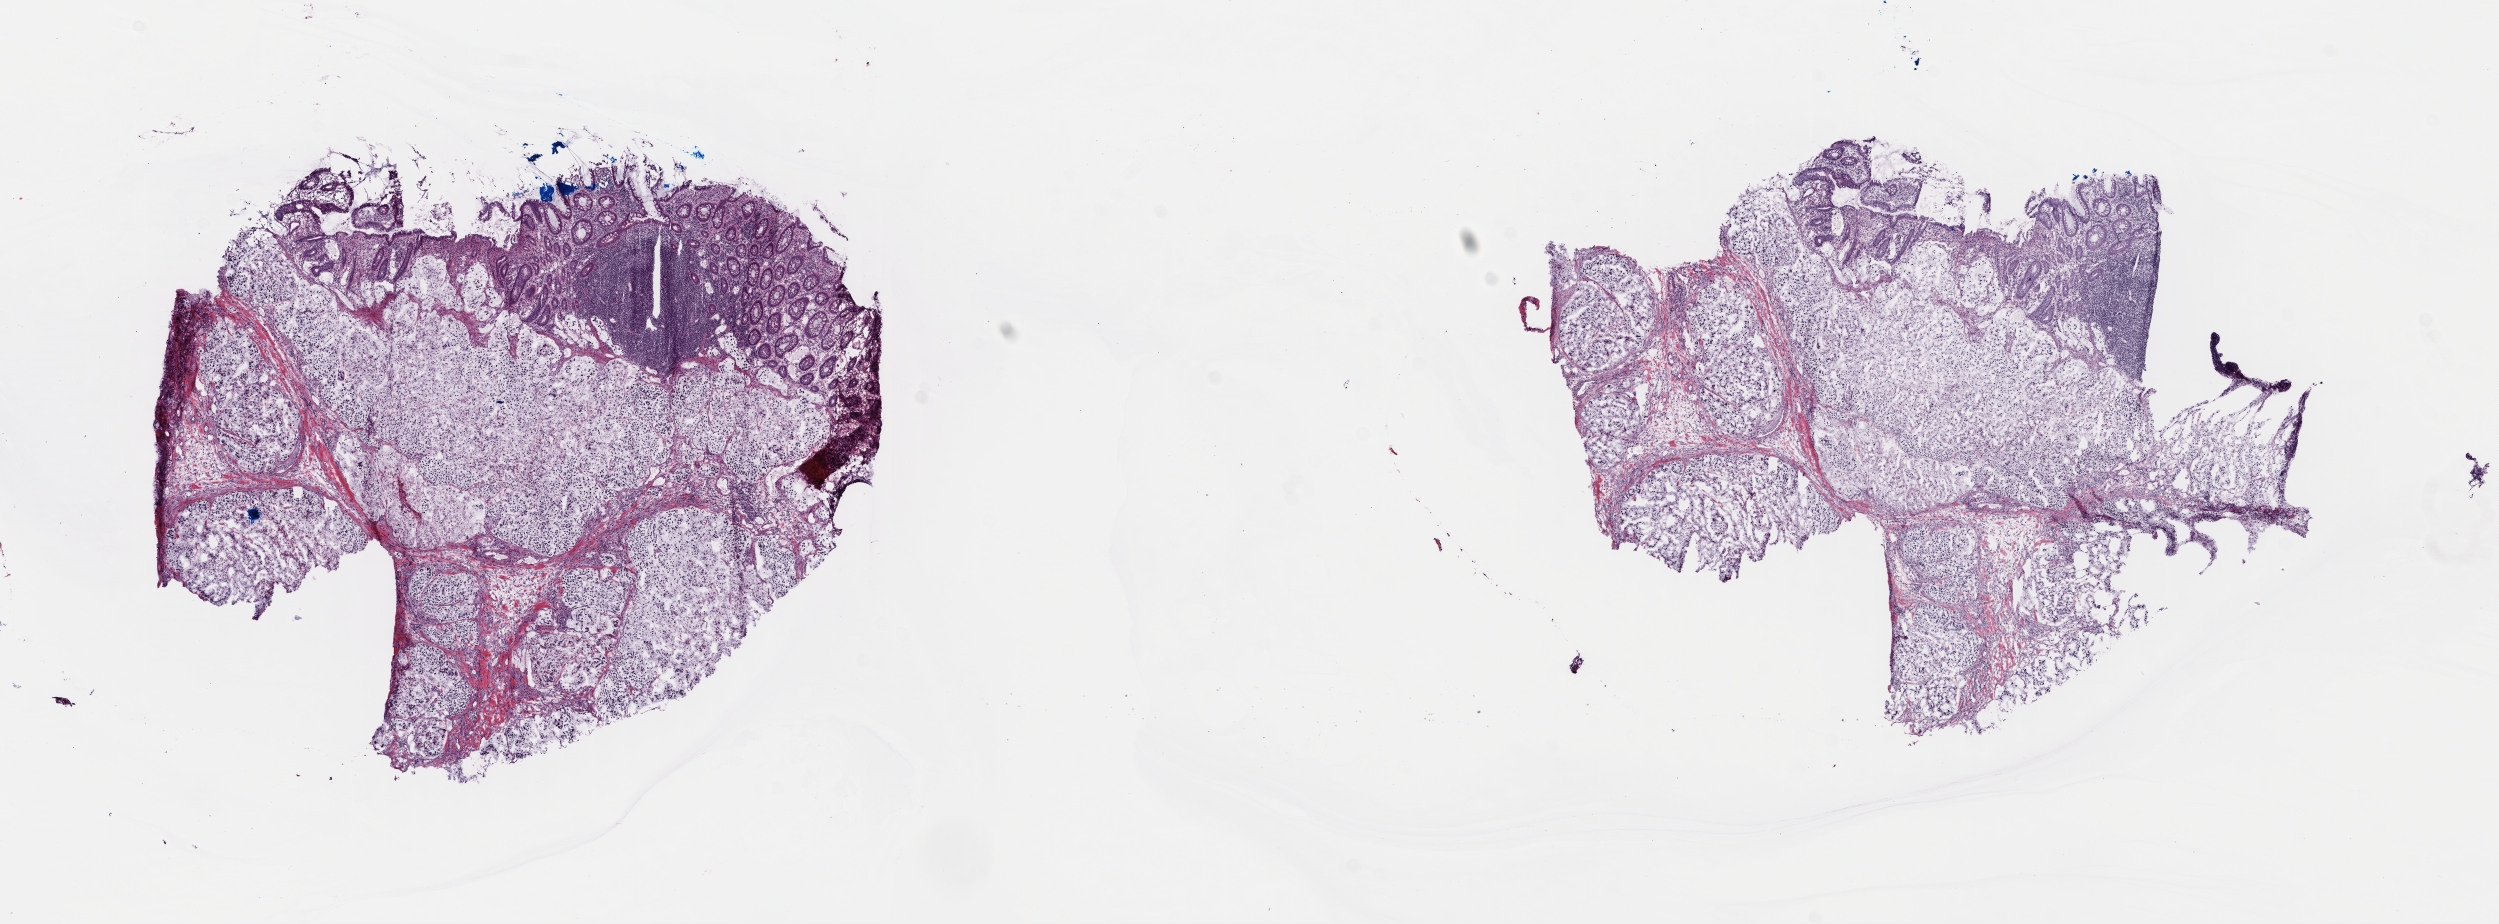
Digitized H&E-stained tissue section (whole slide), shown as a low-resolution overview of the whole scanned area (about 19.6 x 7.3 mm, slide scanned at 40x); frozen section from the top of the tissue portion; sample: primary tumour, colon. Female, age 34 years at initial diagnosis. Slide review estimates, as recorded: tumour cells 65%, tumour nuclei 65%, normal cells 10%, stromal cells 25%, necrosis 0%. Inflammatory infiltration, as recorded: lymphocyte infiltration 7%, monocyte infiltration 1%, neutrophil infiltration 2%.
Pathologic diagnosis: Mucinous adenocarcinoma (transverse colon). AJCC pathologic stage: IIIC.